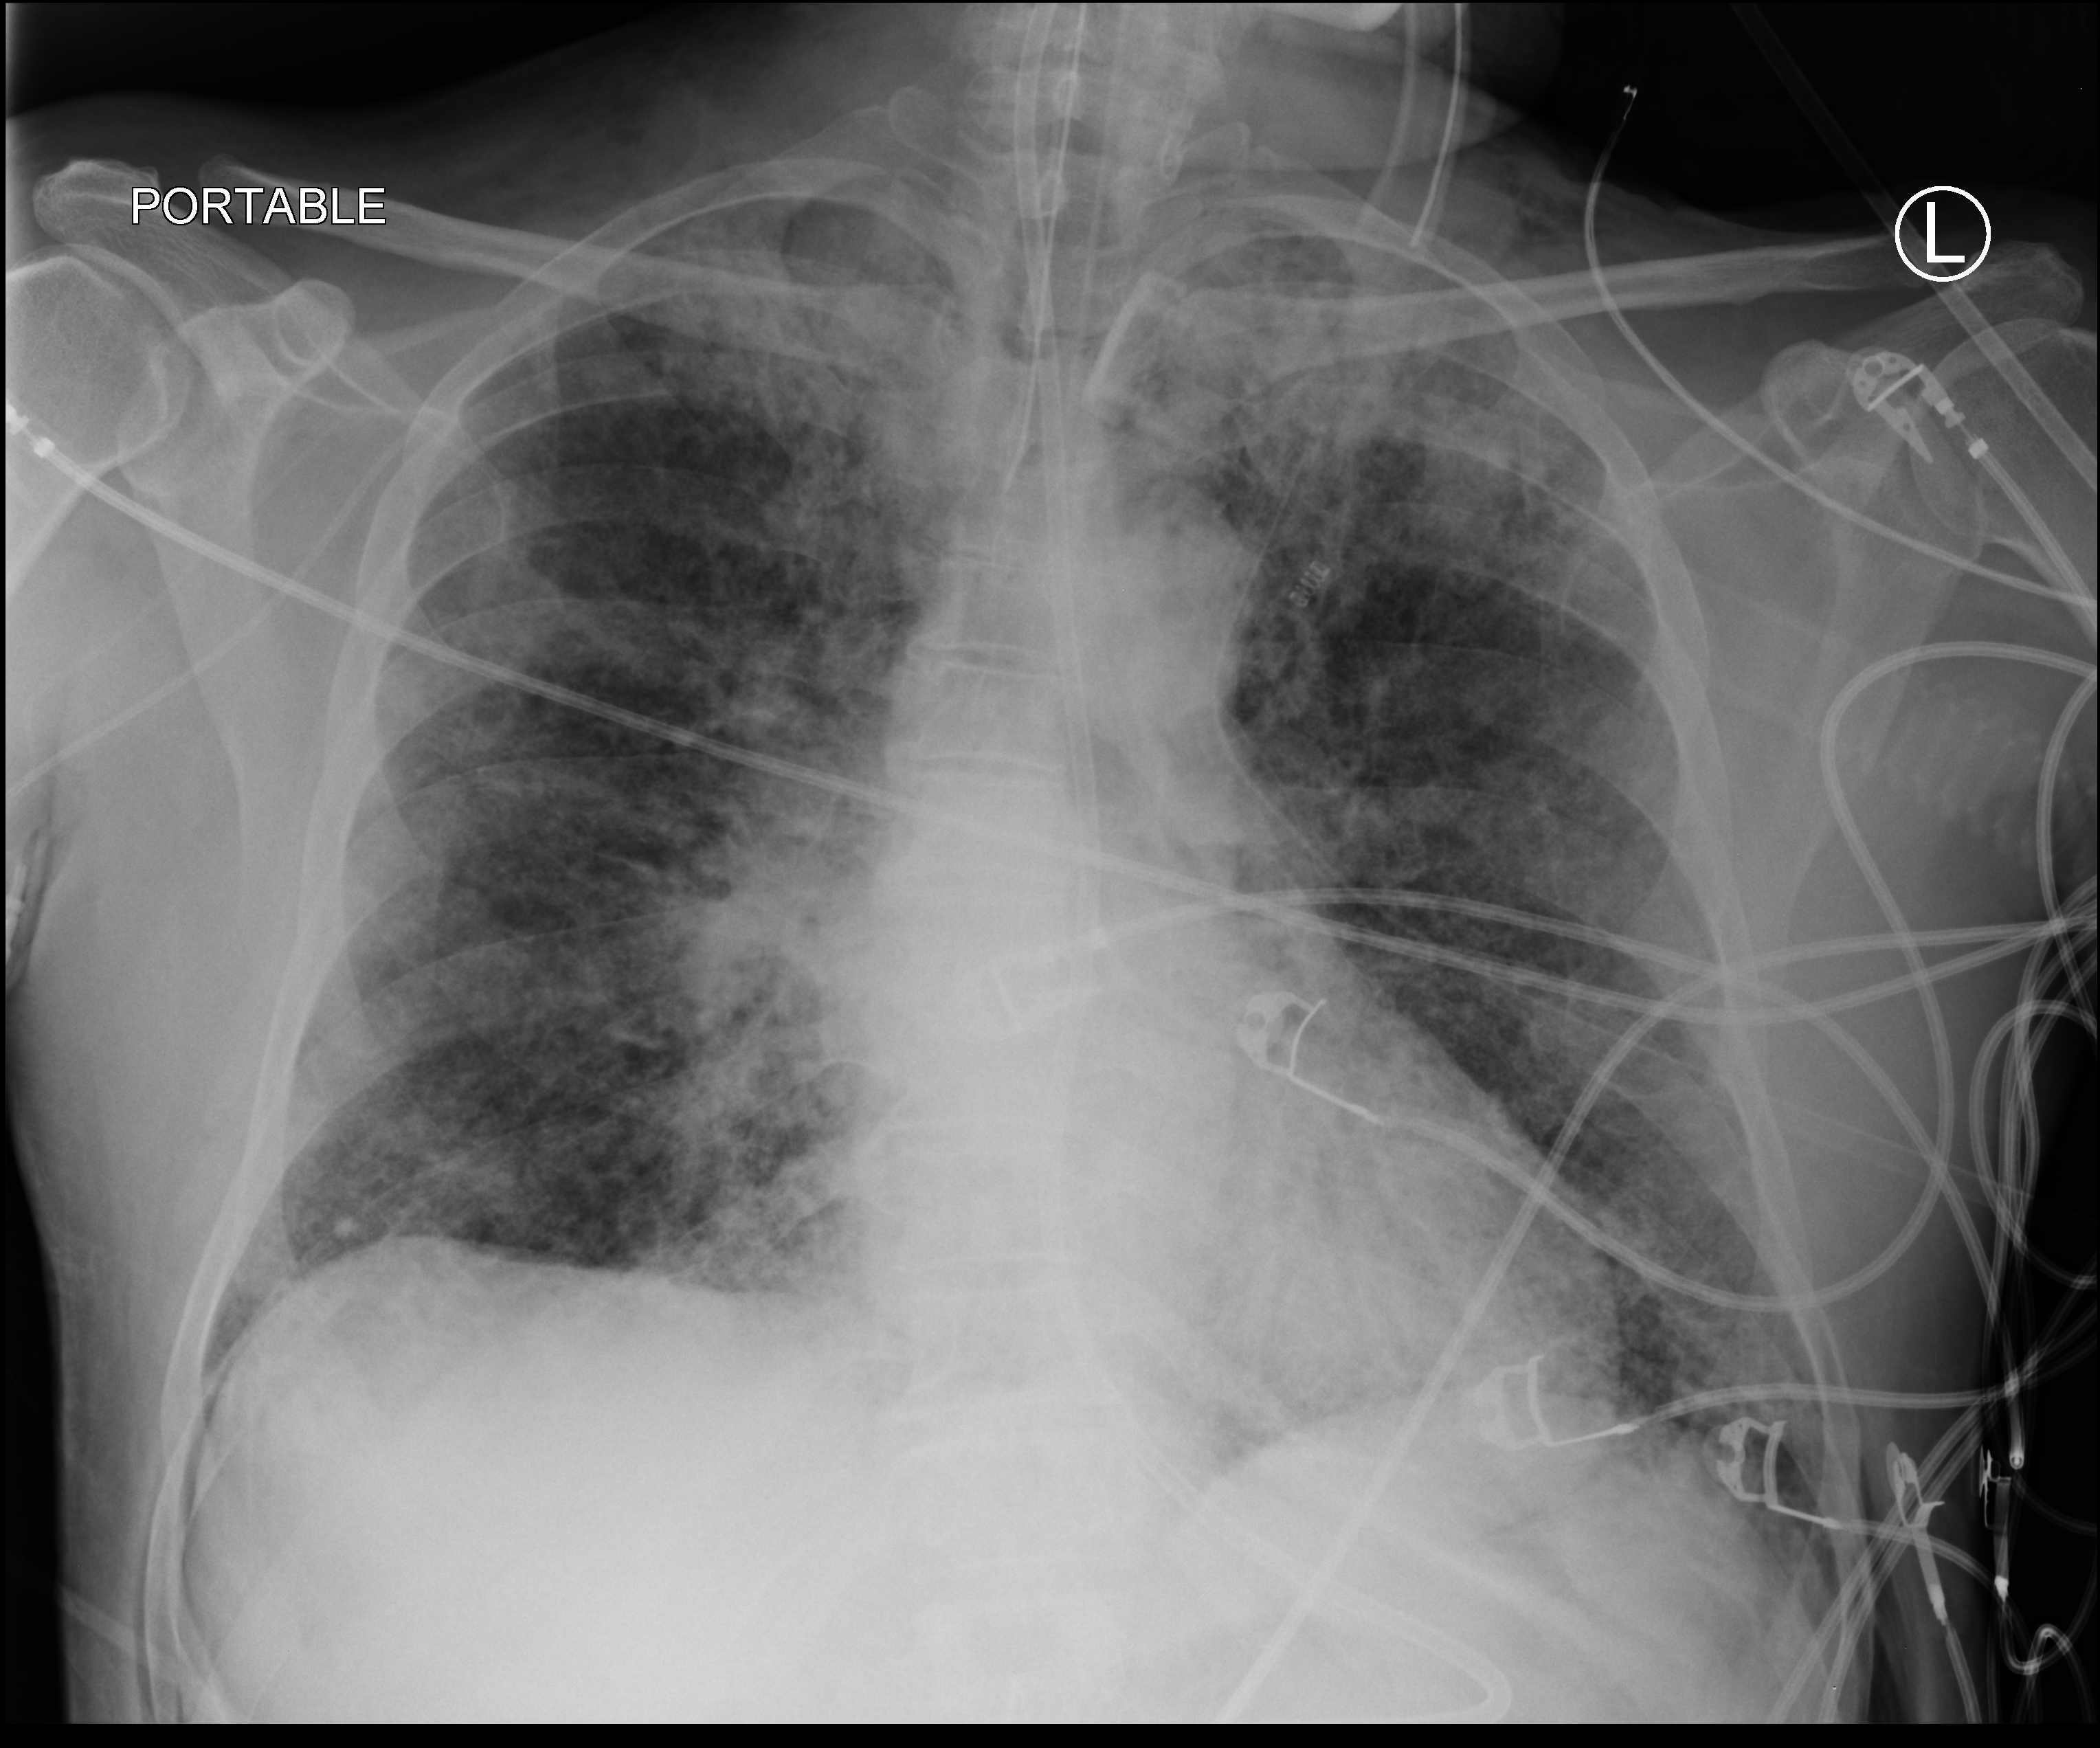
Portable chest radiograph; anteroposterior (AP) projection. Male patient hospitalised with COVID-19, age 18–59 years.
From the hospital-stay record, not from the radiograph (when in the stay this image was taken is not recorded): smoking status (admission record): never; mechanically ventilated during this hospital stay: yes.